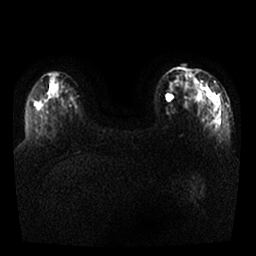
Breast MRI, one axial slice. Slice 7 of 25 in the series (ordered by position). Diffusion-weighted series; image 2 of 4 stored at this slice position (different b-values; order by instance number). 1.5 T. 4 mm slice thickness. 256 × 256 image matrix, field of view 340 × 340 mm. Female patient.
Structures marked on this image (expert manual segmentation):
- tumour on diffusion-weighted imaging: bounding box [x1, y1, x2, y2] px = [193, 95, 221, 126]